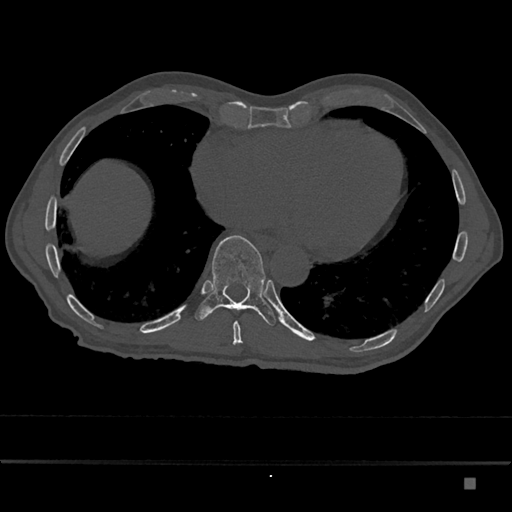
CT including the spine, one axial slice; slice 757 of 797 in the series (ordered by position); 120 kVp; bone window (W 1800 / L 400 HU); 512 × 512 image matrix, field of view 390 × 390 mm. Patient: male, 72 years. Case-level facts recorded for this patient, not image findings: primary cancer: prostate.
Annotated regions visible in this slice (semi-automatically segmented with operator editing):
- T10 vertebra: bounding box [x1, y1, x2, y2] px = [195, 235, 276, 326]
- T9 vertebra: [233, 321, 243, 345]